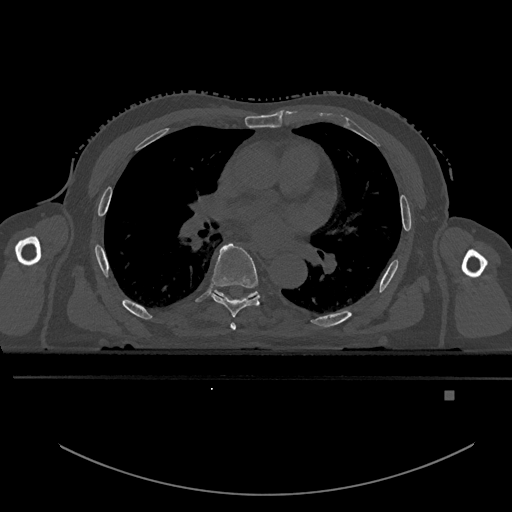
CT including the spine, one axial slice; bone window (W 1800 / L 400 HU); 0.5 mm slice thickness; 512 × 512 image matrix, field of view 456 × 456 mm. Male patient, age 82 years. From the clinical record (not read from this slice): primary cancer: prostate.
Structures marked on this image (semi-automatic segmentation, software-assisted and operator-edited):
- T5 vertebra: bounding box (x1, y1, x2, y2) in pixels: (230, 322, 236, 330)
- T6 vertebra: (212, 242, 261, 317)
- T7 vertebra: (215, 291, 256, 298)